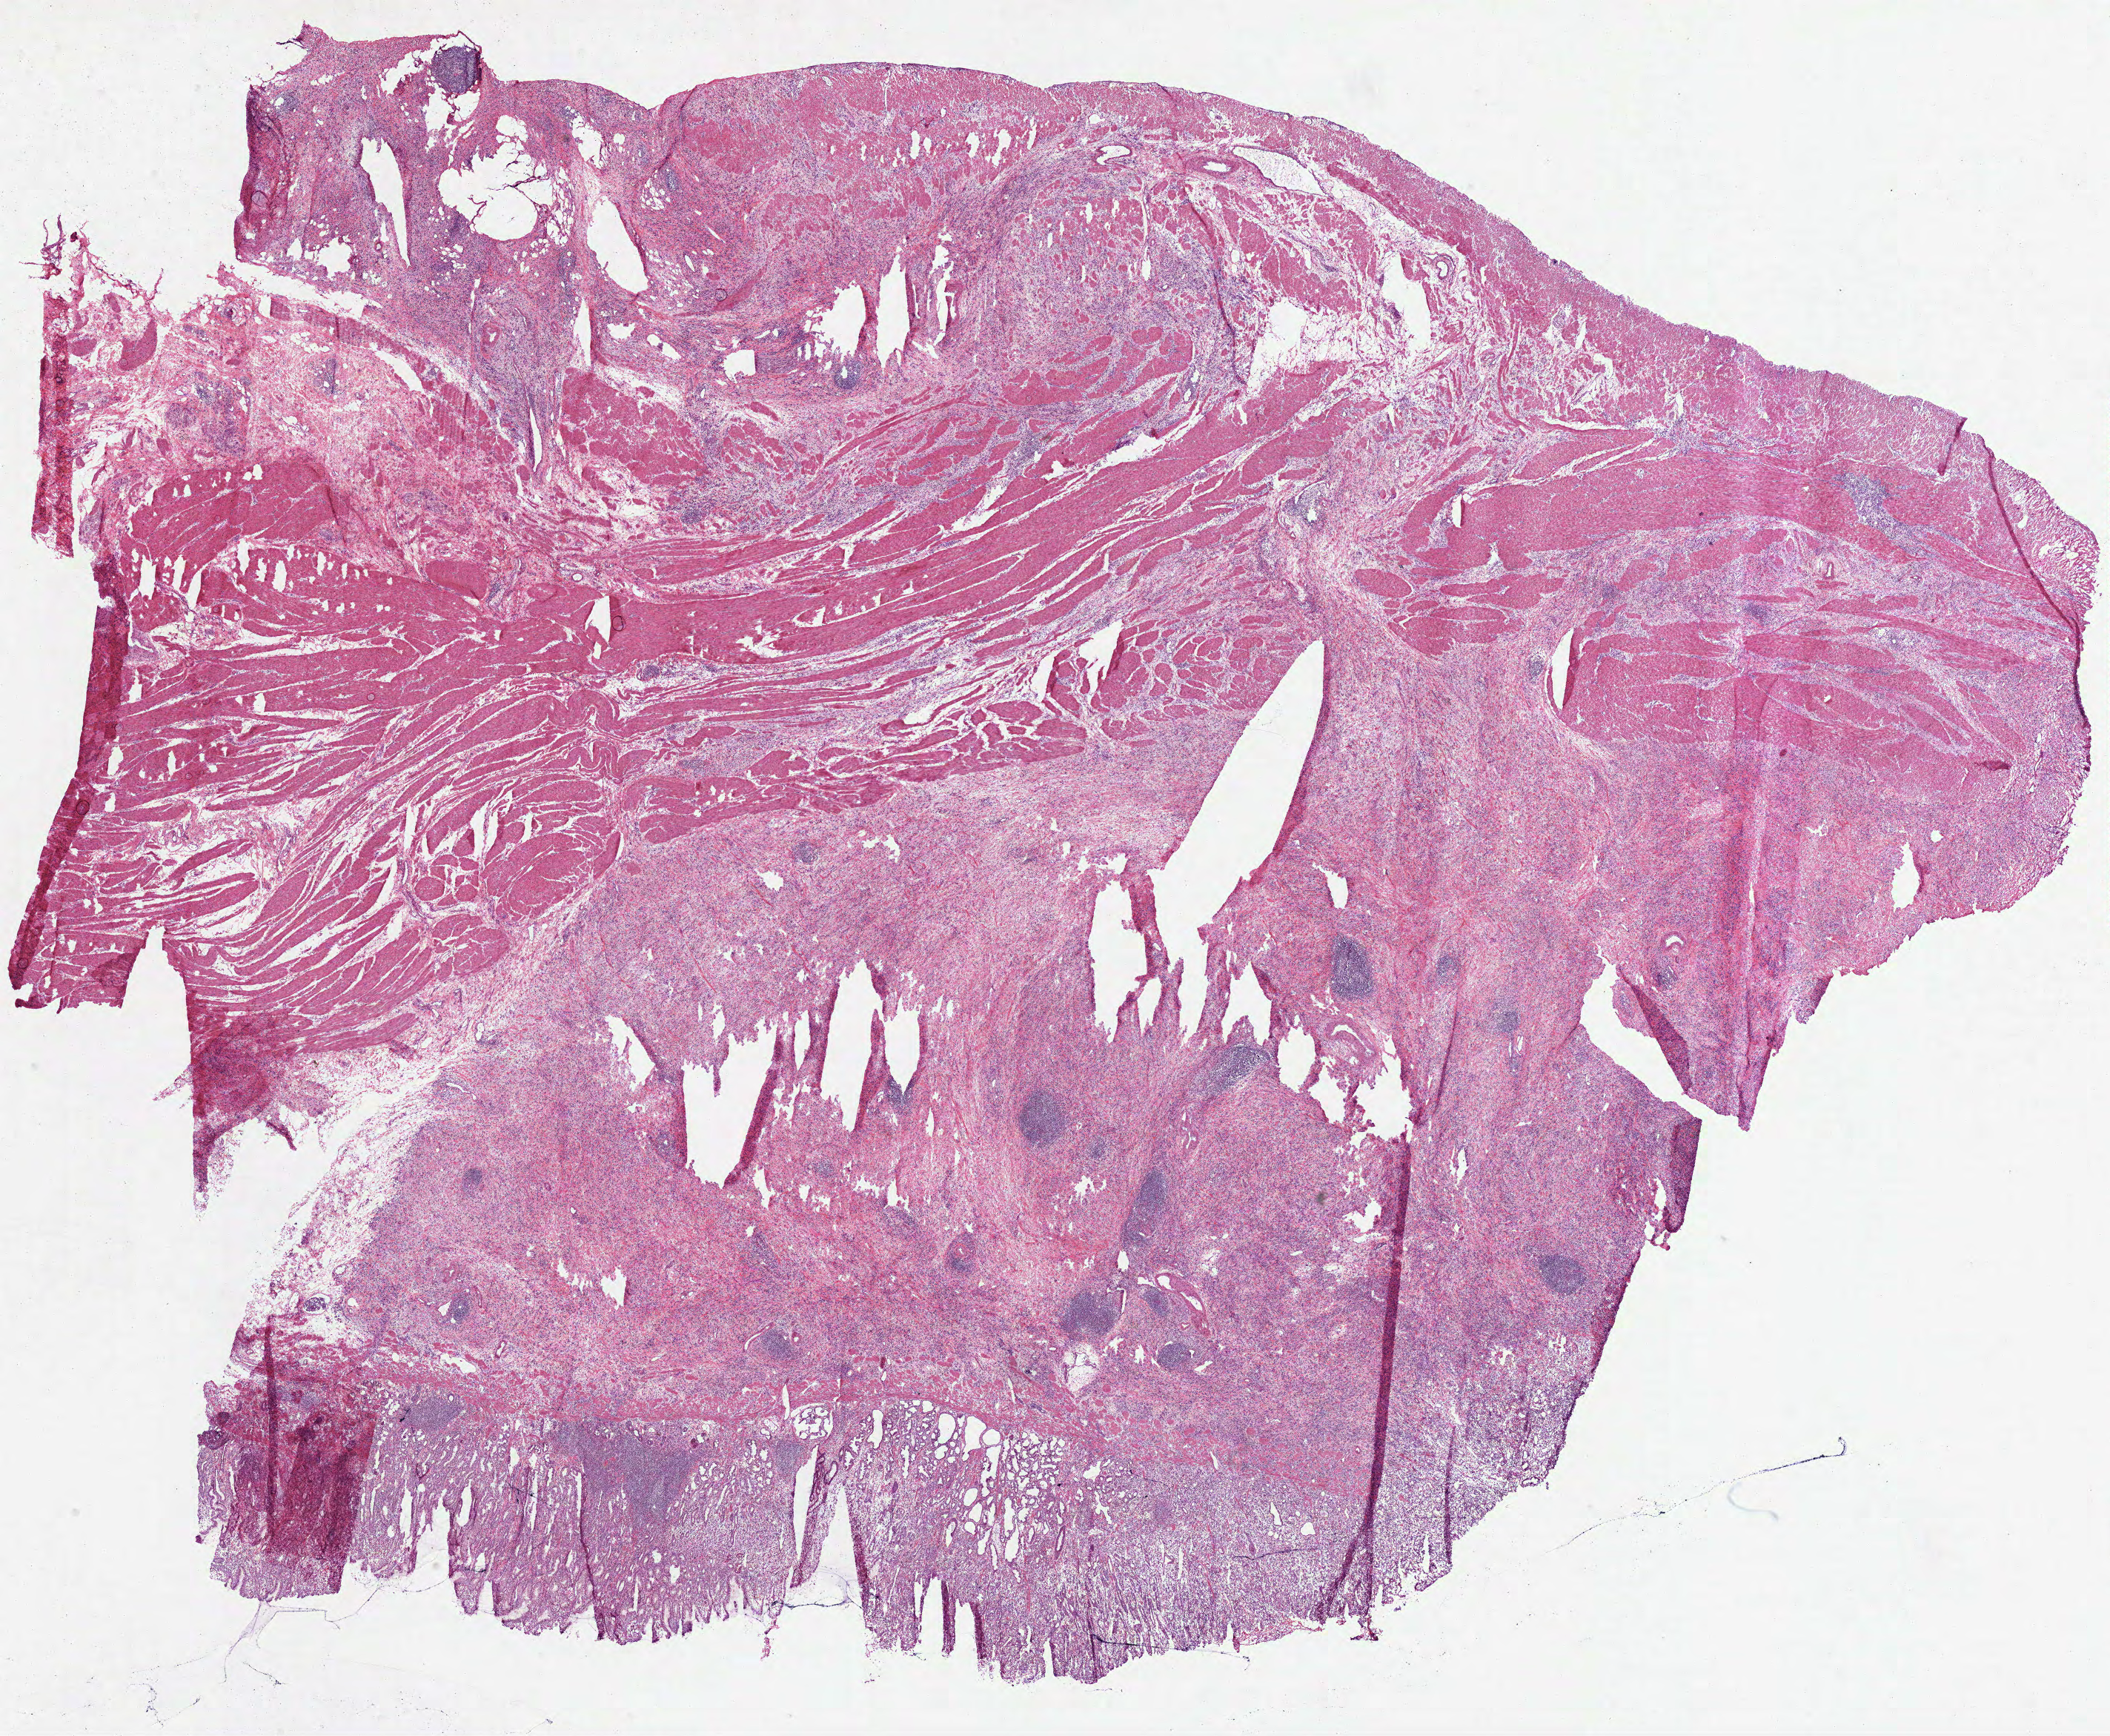
Digitized H&E tissue section (whole slide), low-resolution overview of the scanned area, about 23.0 x 18.9 mm (acquisition: 40x scan); frozen section; primary tumour sample from the stomach. Patient: male, age at initial diagnosis 69 years. Histologic grade: G3 (poorly differentiated). Slide review estimates, as recorded: tumour cells 50%, tumour nuclei 60%, normal cells 30%, stromal cells 20%, necrosis 0%. Infiltration values recorded for this section: lymphocyte infiltration 20%.
Lymph nodes positive (case pathology): 6 of 18 examined. Pathologic diagnosis: Adenocarcinoma, NOS. AJCC pathologic stage: IIIC.